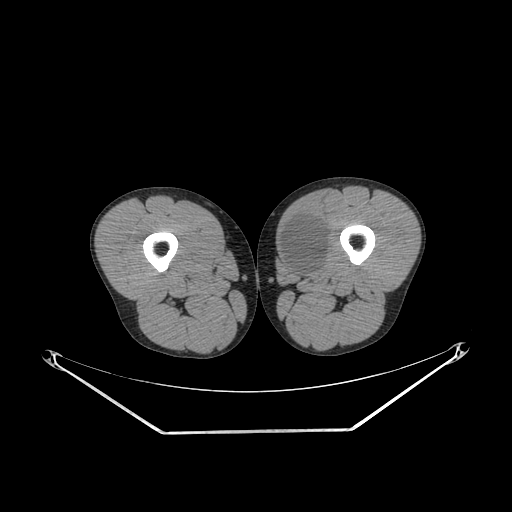
CT of an extremity soft-tissue mass (from a PET/CT study), one axial slice. 140 kVp. Soft-tissue window (W 400 / L 40 HU). 3.75 mm slice thickness. 512 × 512 image matrix, field of view 500 × 500 mm. Male patient. Case-level facts recorded for this patient, not image findings: histological type: mixoid liposarcoma; grade: low; site of the primary tumour: left thigh.
Structures marked on this image (expert contour drawn on MRI and transferred to this co-registered scan by the dataset authors):
- gross tumour volume (mass): bounding box <279,215,328,275> (left, top, right, bottom; pixels)